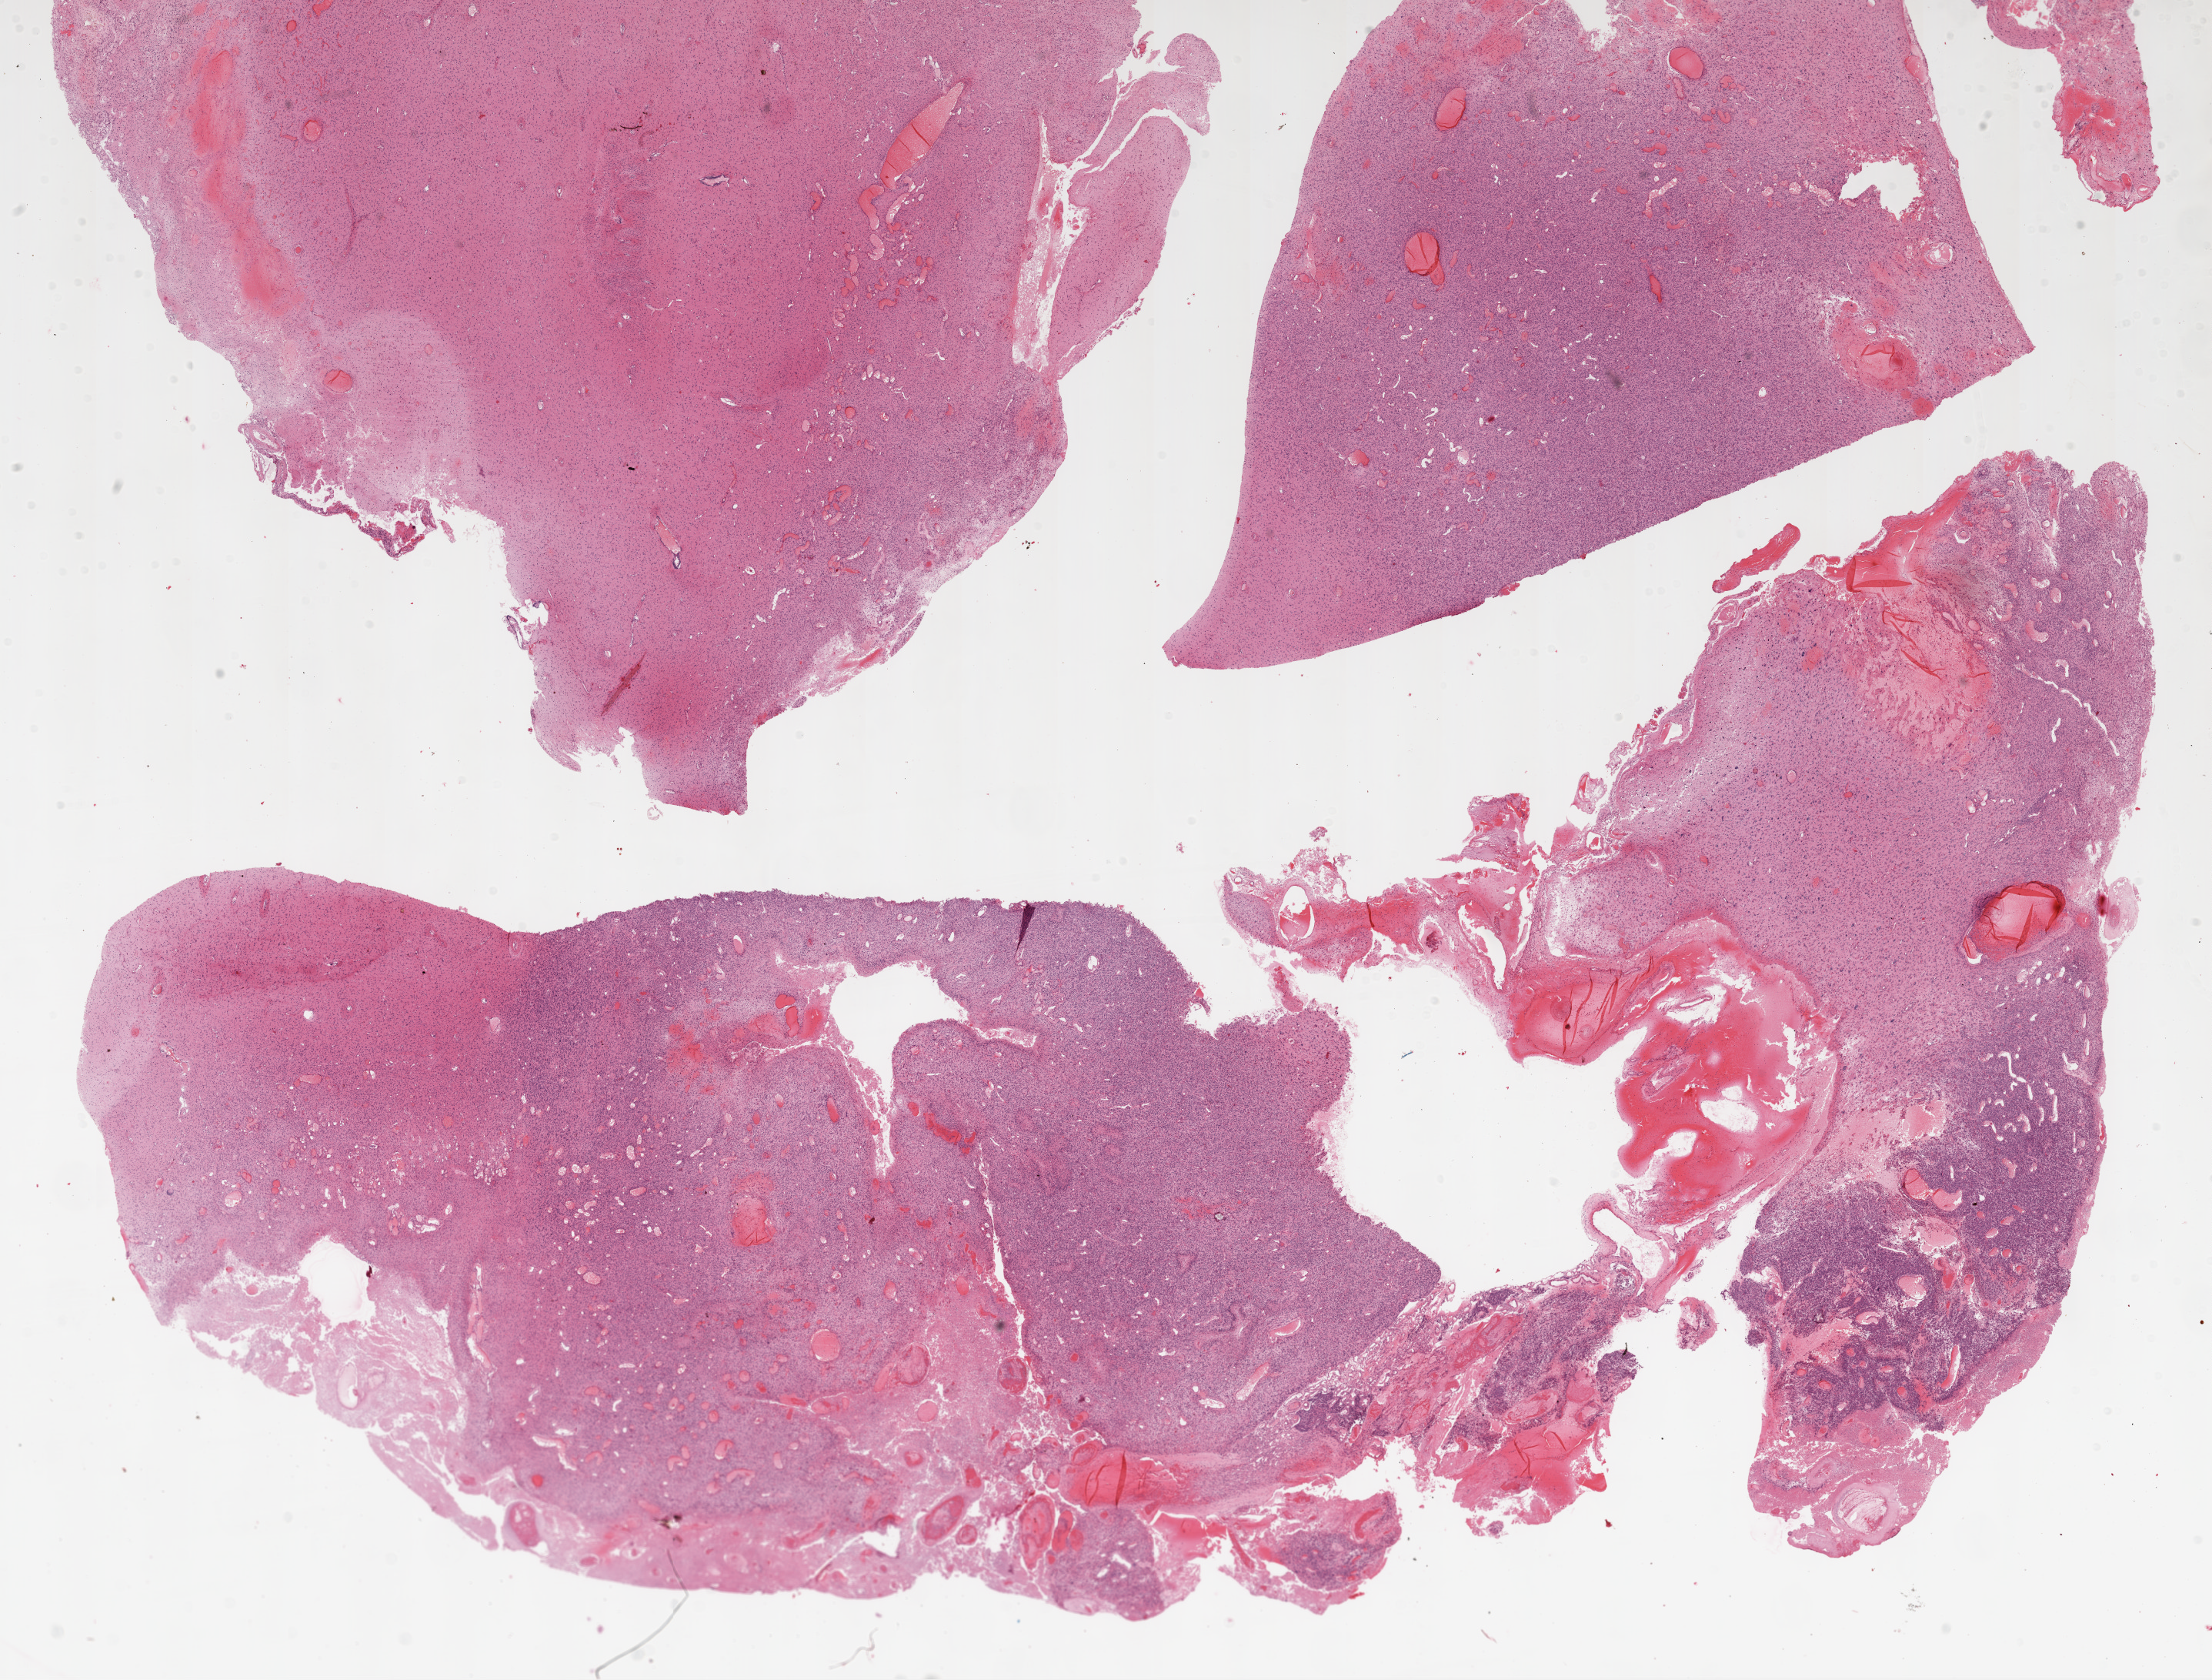
Hematoxylin and eosin (H&E) stained whole-slide image, whole scanned area (about 23.1 x 17.5 mm, slide scanned at 20x) shown as a low-resolution overview. Formalin-fixed paraffin-embedded (FFPE) diagnostic section. Sample: primary tumour, brain. Patient: female, age at initial diagnosis 33 years.
Diagnosis: Glioblastoma.